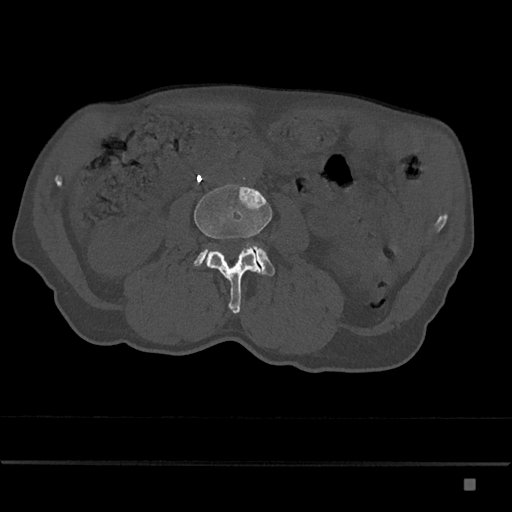
CT including the spine, one axial slice. Slice 387 of 797 in the series (ordered by position). Reconstruction kernel Br40s/3. Bone window (W 1800 / L 400 HU). 0.5 mm slice thickness. 512 × 512 image matrix, field of view 390 × 390 mm. Patient: male, 72 years. Case-level facts recorded for this patient, not image findings: primary cancer: prostate.
Annotated regions visible in this slice (semi-automatic segmentation, software-assisted and operator-edited):
- L3 vertebra: box from (x=194, y=184) to (x=272, y=314) px
- L4 vertebra: (x=194, y=244)–(x=275, y=276)